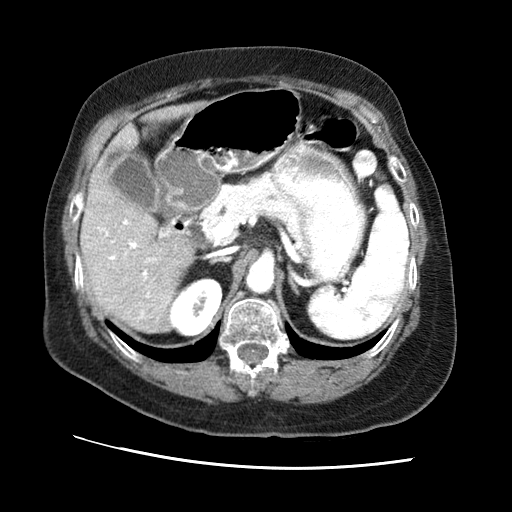
Contrast-enhanced abdominal CT (liver protocol), one axial slice; position 33 of 65 along the scan axis; 120 kVp; soft-tissue window (W 400 / L 40 HU); 2.5 mm slice thickness; 512 × 512 image matrix, field of view 340 × 340 mm. From the clinical record (not read from this slice): diagnosis: hepatocellular carcinoma (patient treated with transarterial chemoembolisation; whether this scan precedes or follows treatment is not stated here); TNM stage (as recorded): Stage-II; Child-Pugh class: A; tumour nodularity: multinodular; tumour size: 2.5 cm.
Annotated regions visible in this slice (semi-automatic segmentation, software-assisted and operator-edited):
- liver parenchyma outside the tumour (the mass and vessels are separate outlines, so this box may not span the whole liver): bounding box [x1, y1, x2, y2] px = [80, 106, 192, 332]
- liver vessels: [99, 219, 167, 319]